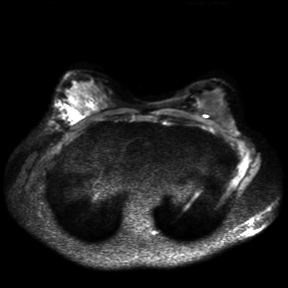
Breast MRI, one axial slice; position 20 of 30 along the scan axis; diffusion-weighted series; image 2 of 4 stored at this slice position (different b-values; order by instance number); 3 T; 4 mm slice thickness; 288 × 288 image matrix. Female patient.
Structures marked on this image (manually delineated by an expert):
- tumour on diffusion-weighted imaging: box from (x=66, y=108) to (x=80, y=122) px